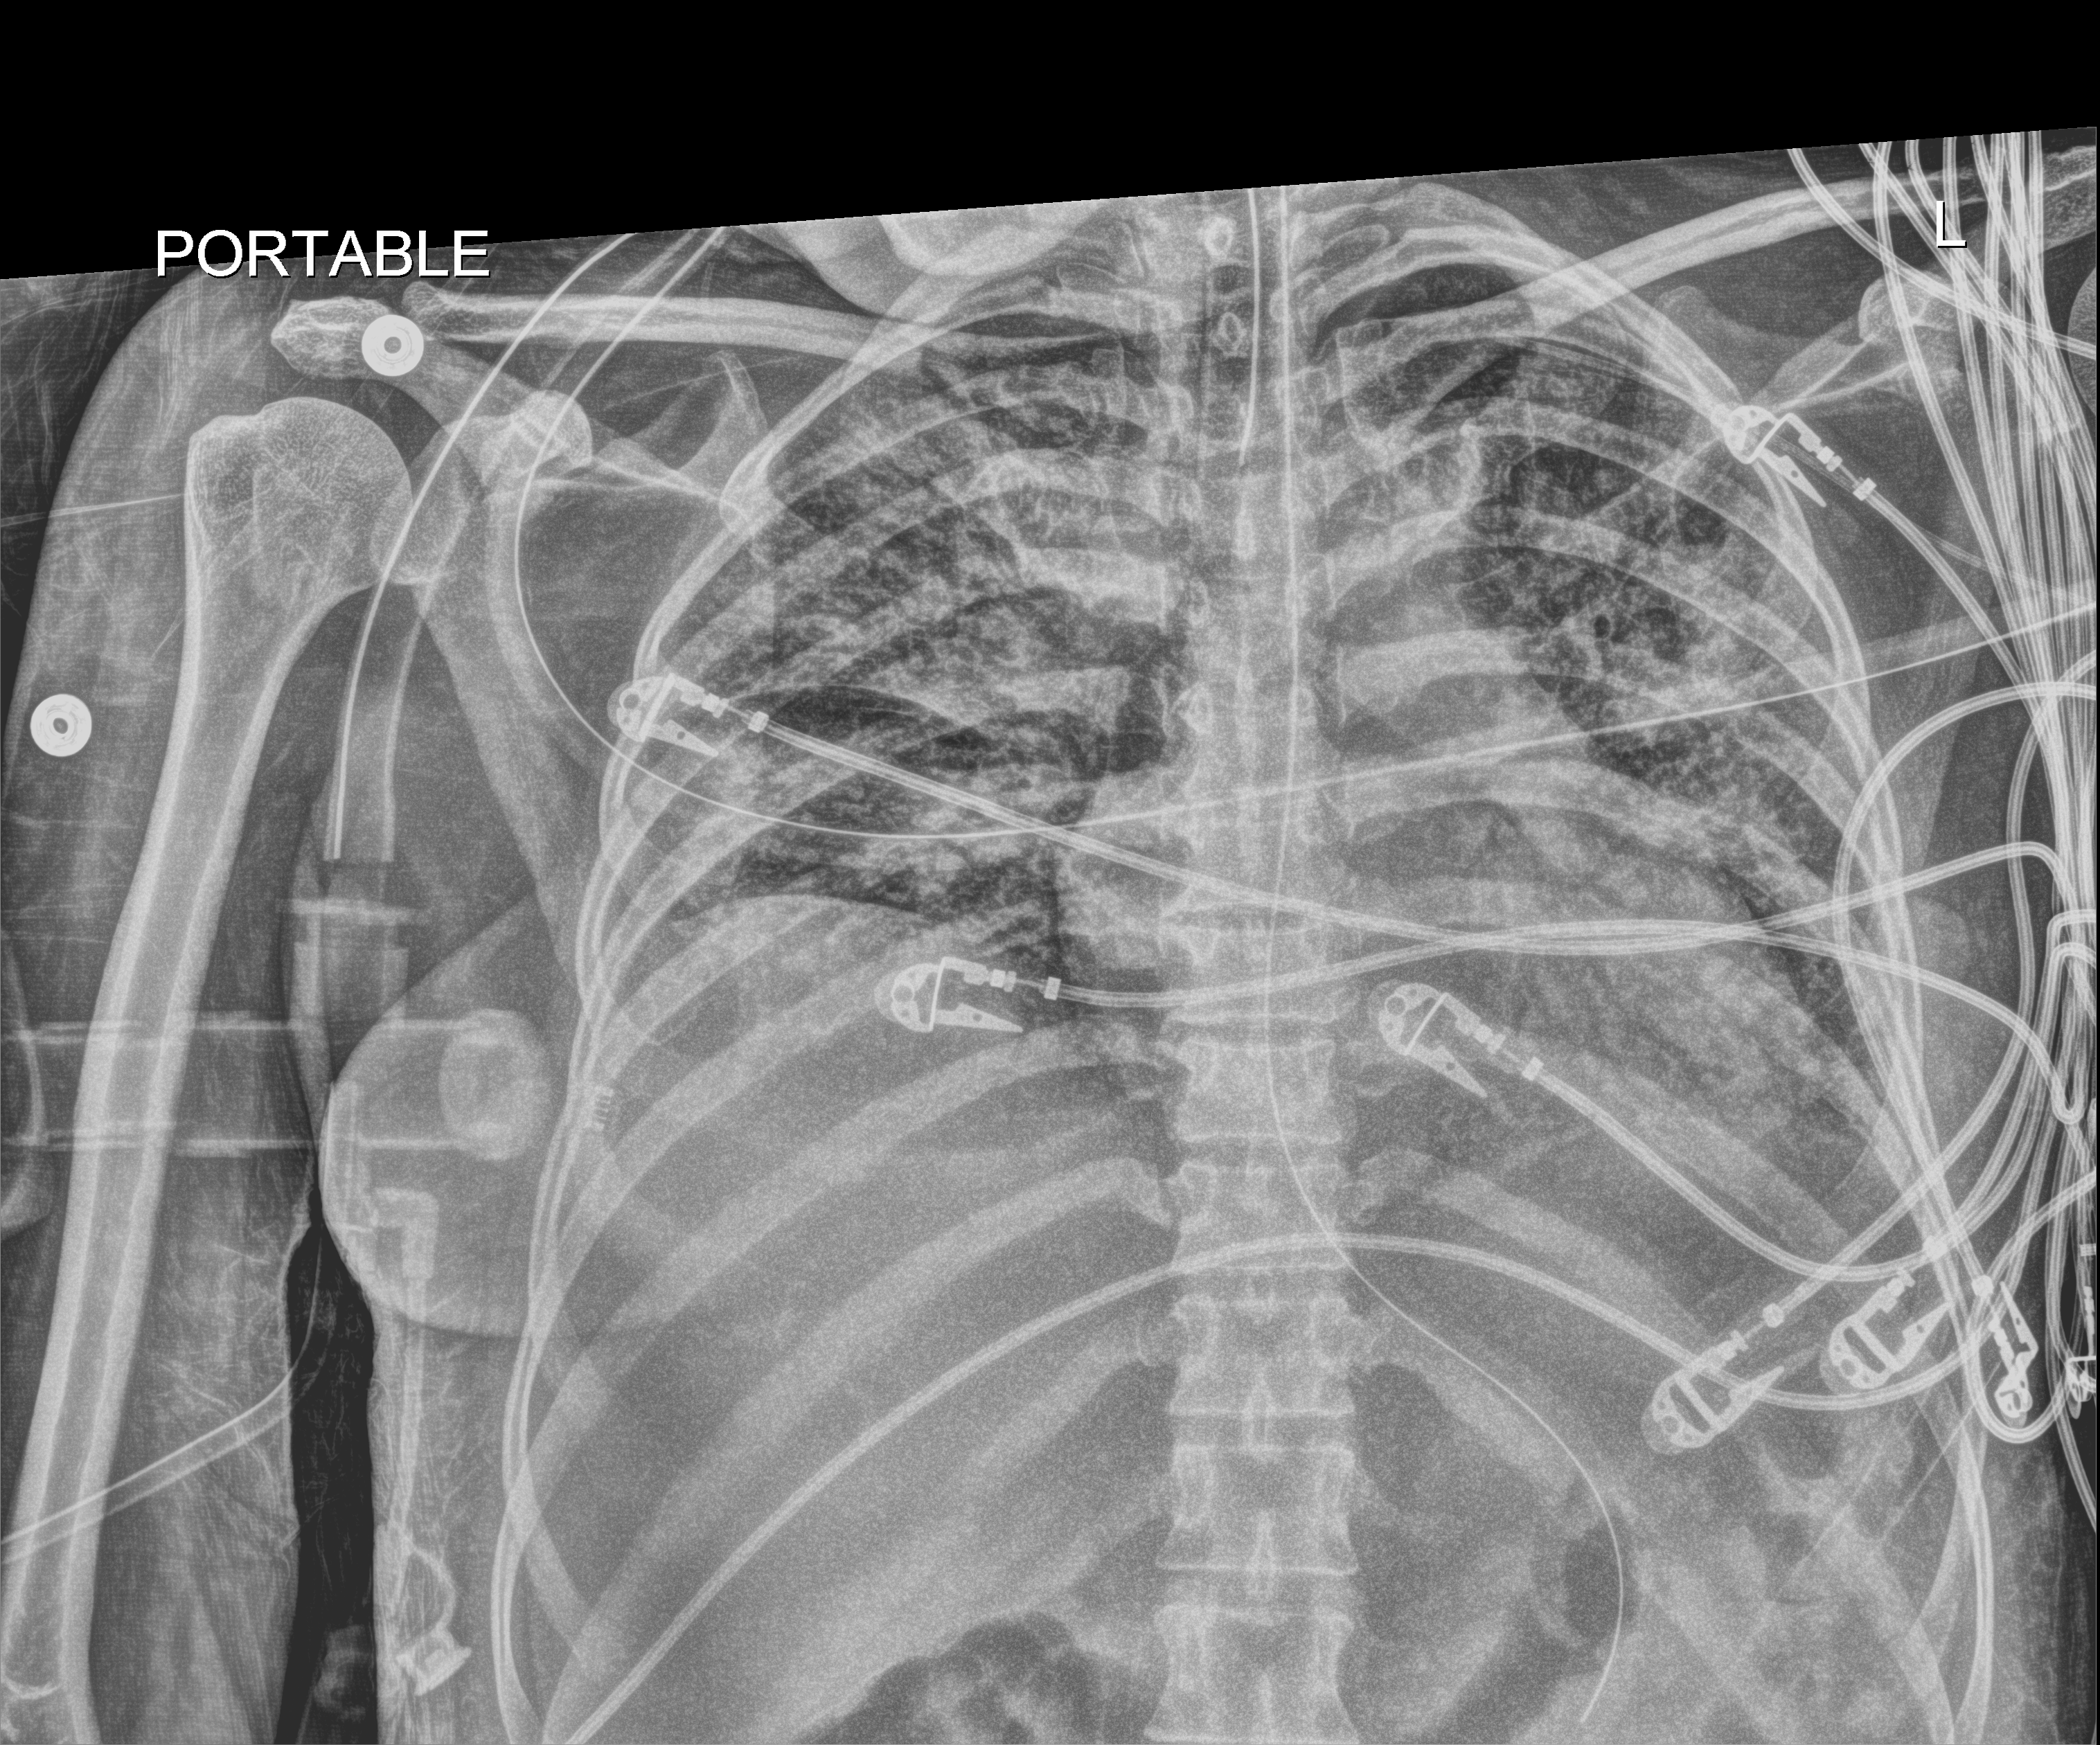
Chest X-ray (portable); anteroposterior (AP) projection. Patient hospitalised with COVID-19; female, aged 18–59 years.
From the hospital-stay record, not from the radiograph (when in the stay this image was taken is not recorded):
- mechanically ventilated during this hospital stay: yes